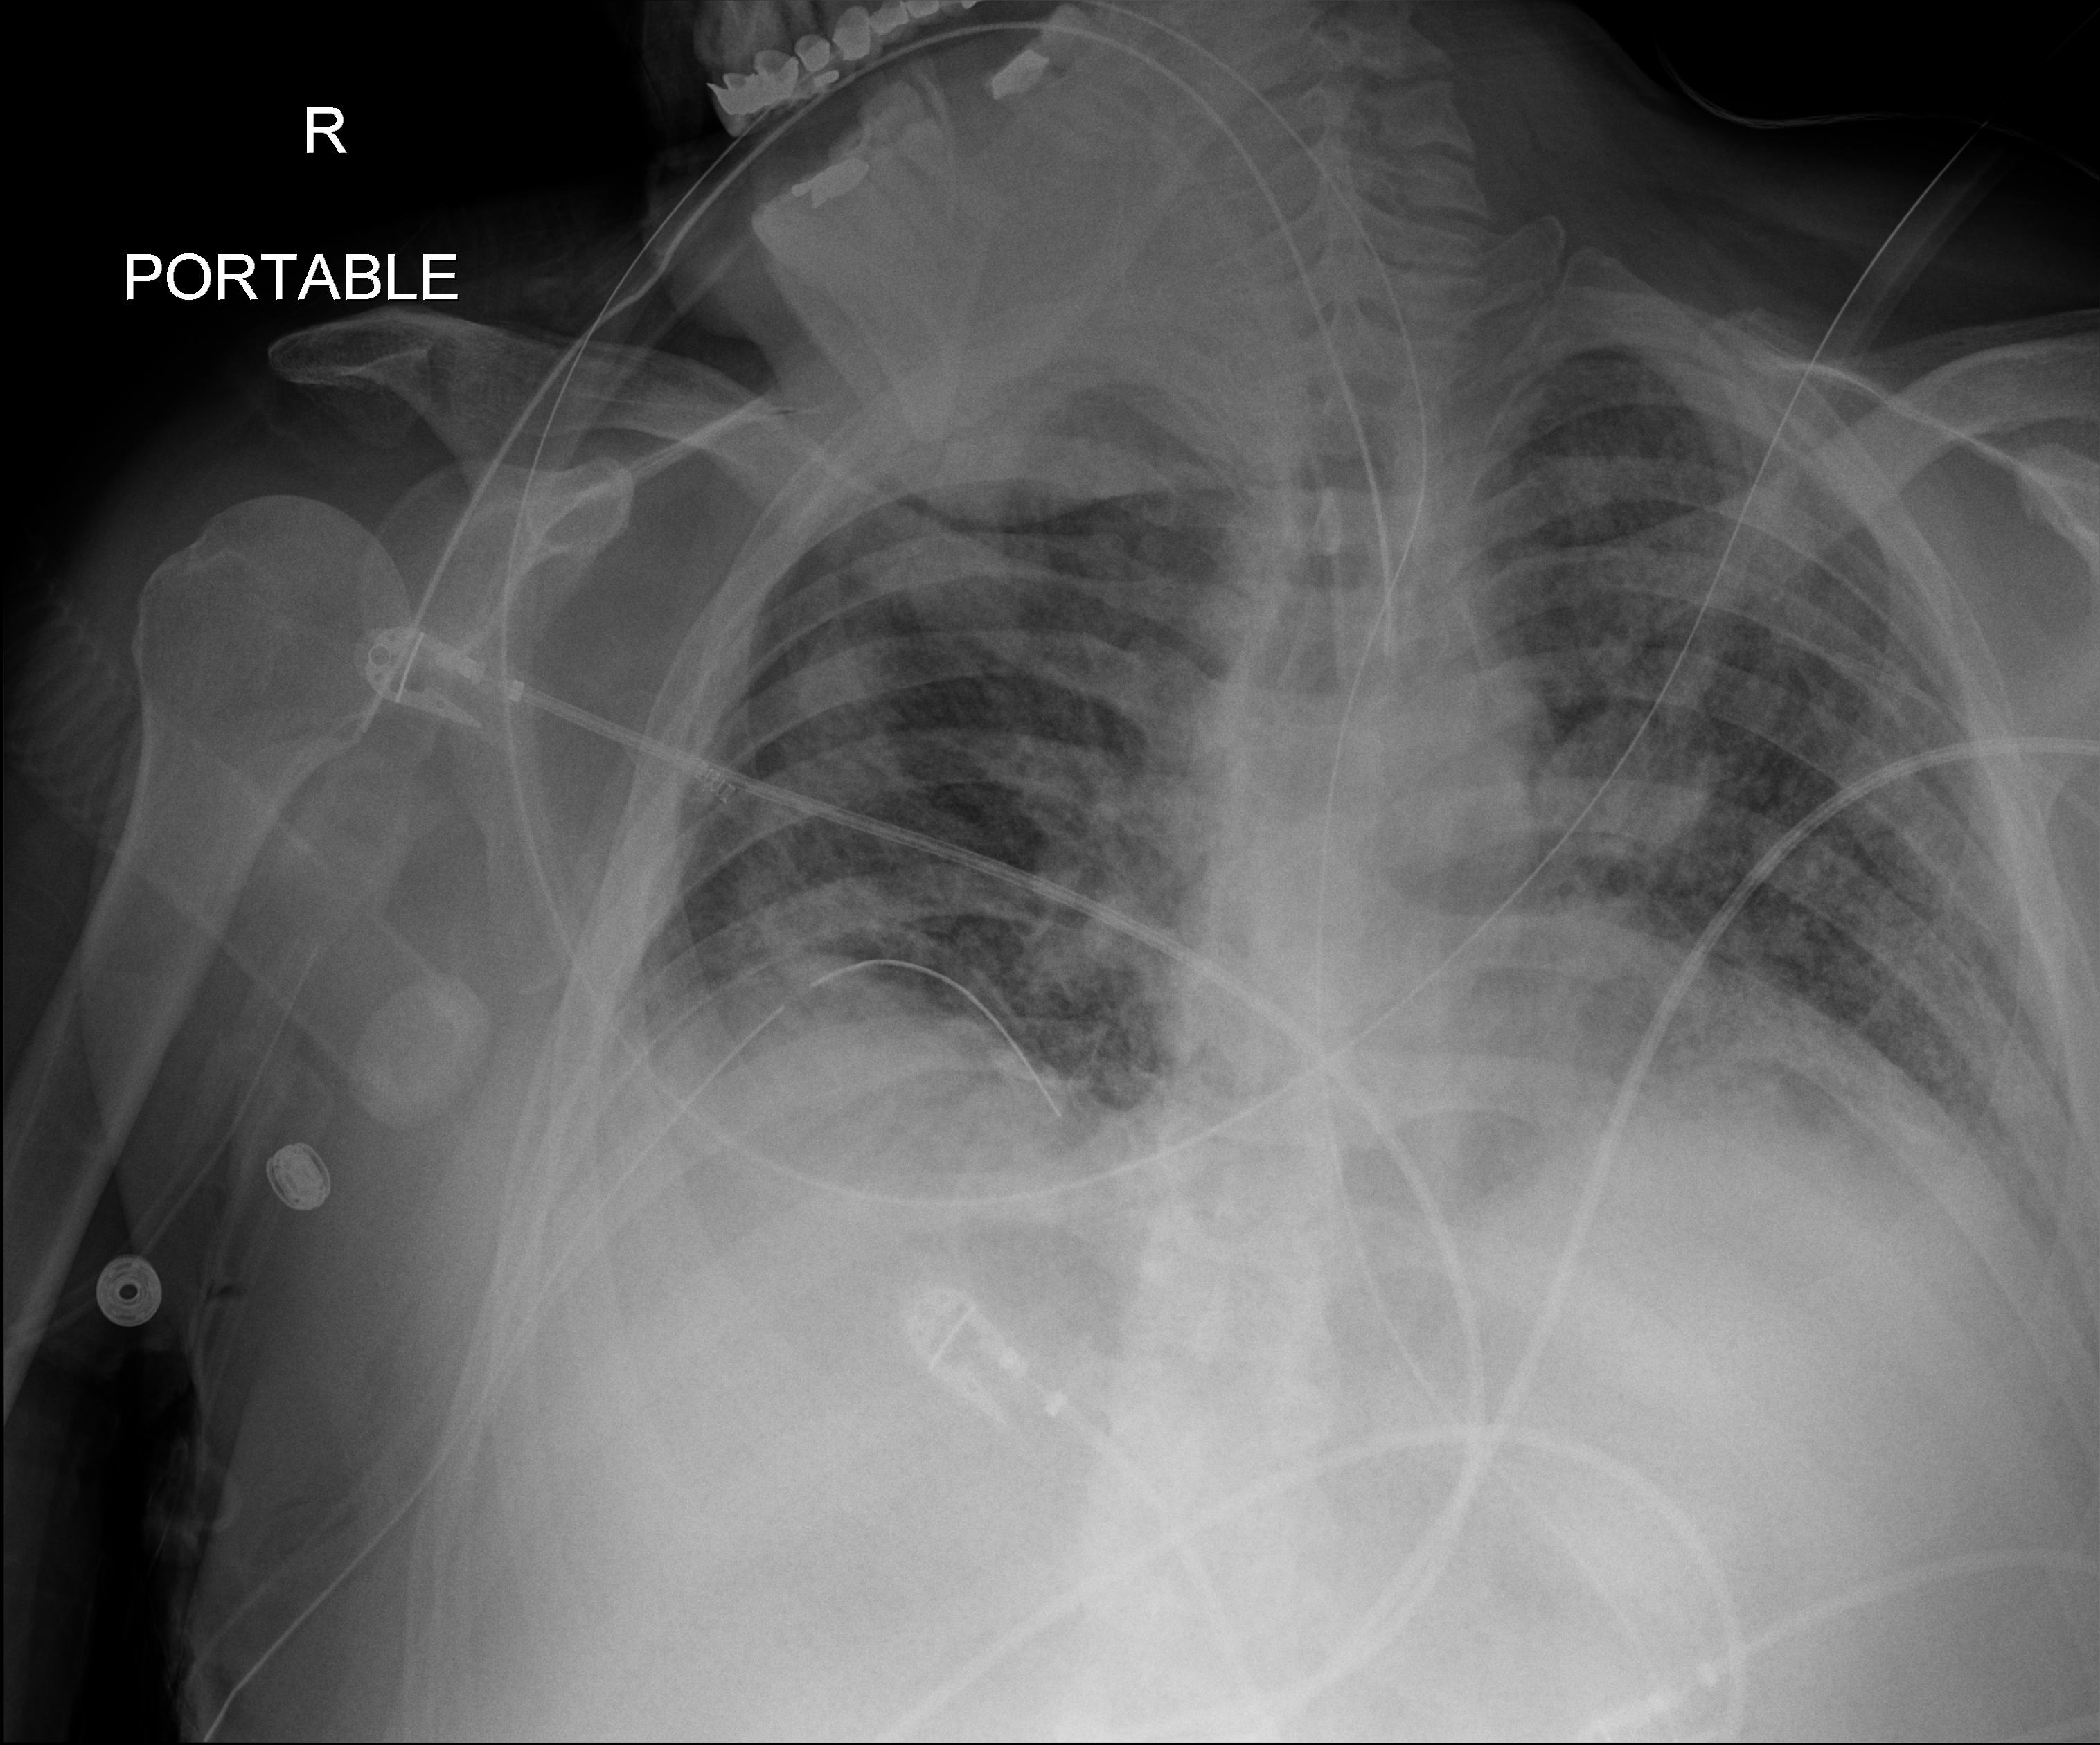
Chest X-ray; anteroposterior (AP) projection. Patient hospitalised with COVID-19; male, aged 18–59 years.
Hospital-stay facts (about this admission, not read from this image; timing relative to this image not recorded): admitted to intensive care during this hospital stay: yes.